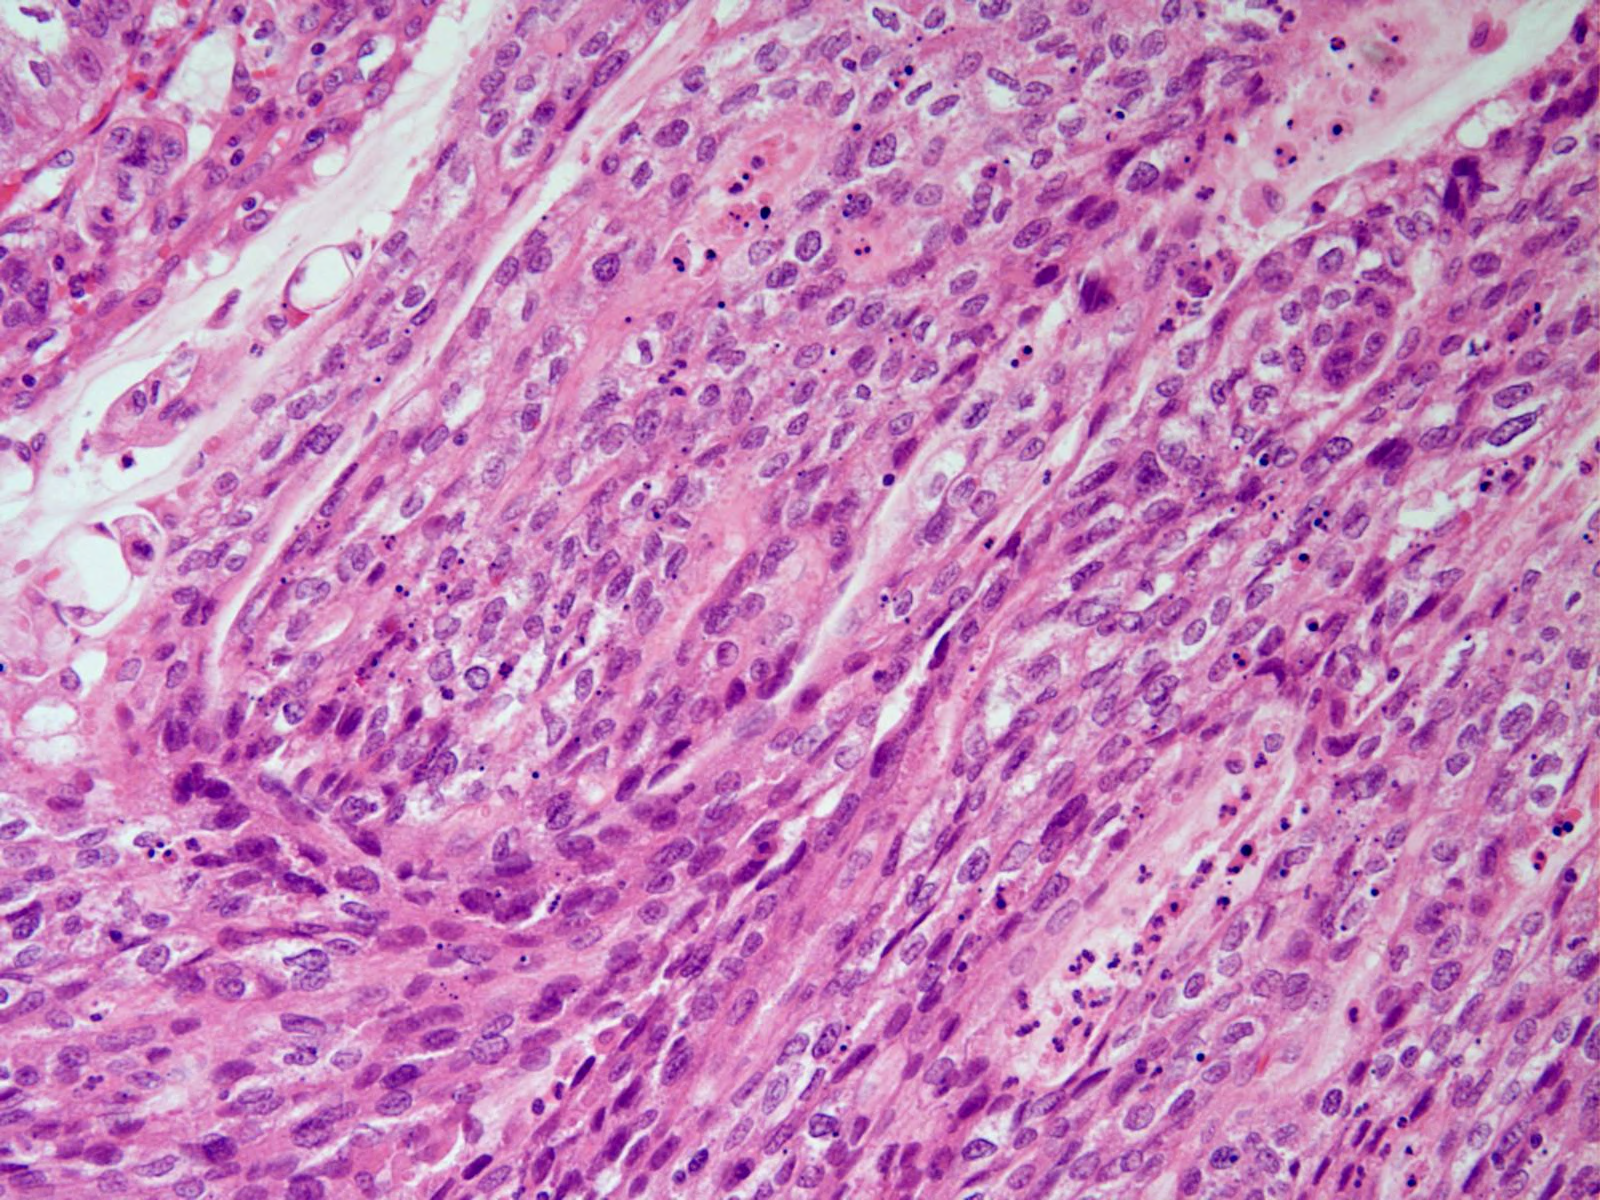
H&E-stained micrograph of a single small tissue field — covering about 0.8 x 0.6 mm; formalin-fixed paraffin-embedded (FFPE) diagnostic section; primary tumour sample from the stomach. Patient: female, age at initial diagnosis 79 years. Histologic grade: G2 (moderately differentiated).
* histologic diagnosis: Adenocarcinoma, NOS (gastric antrum)